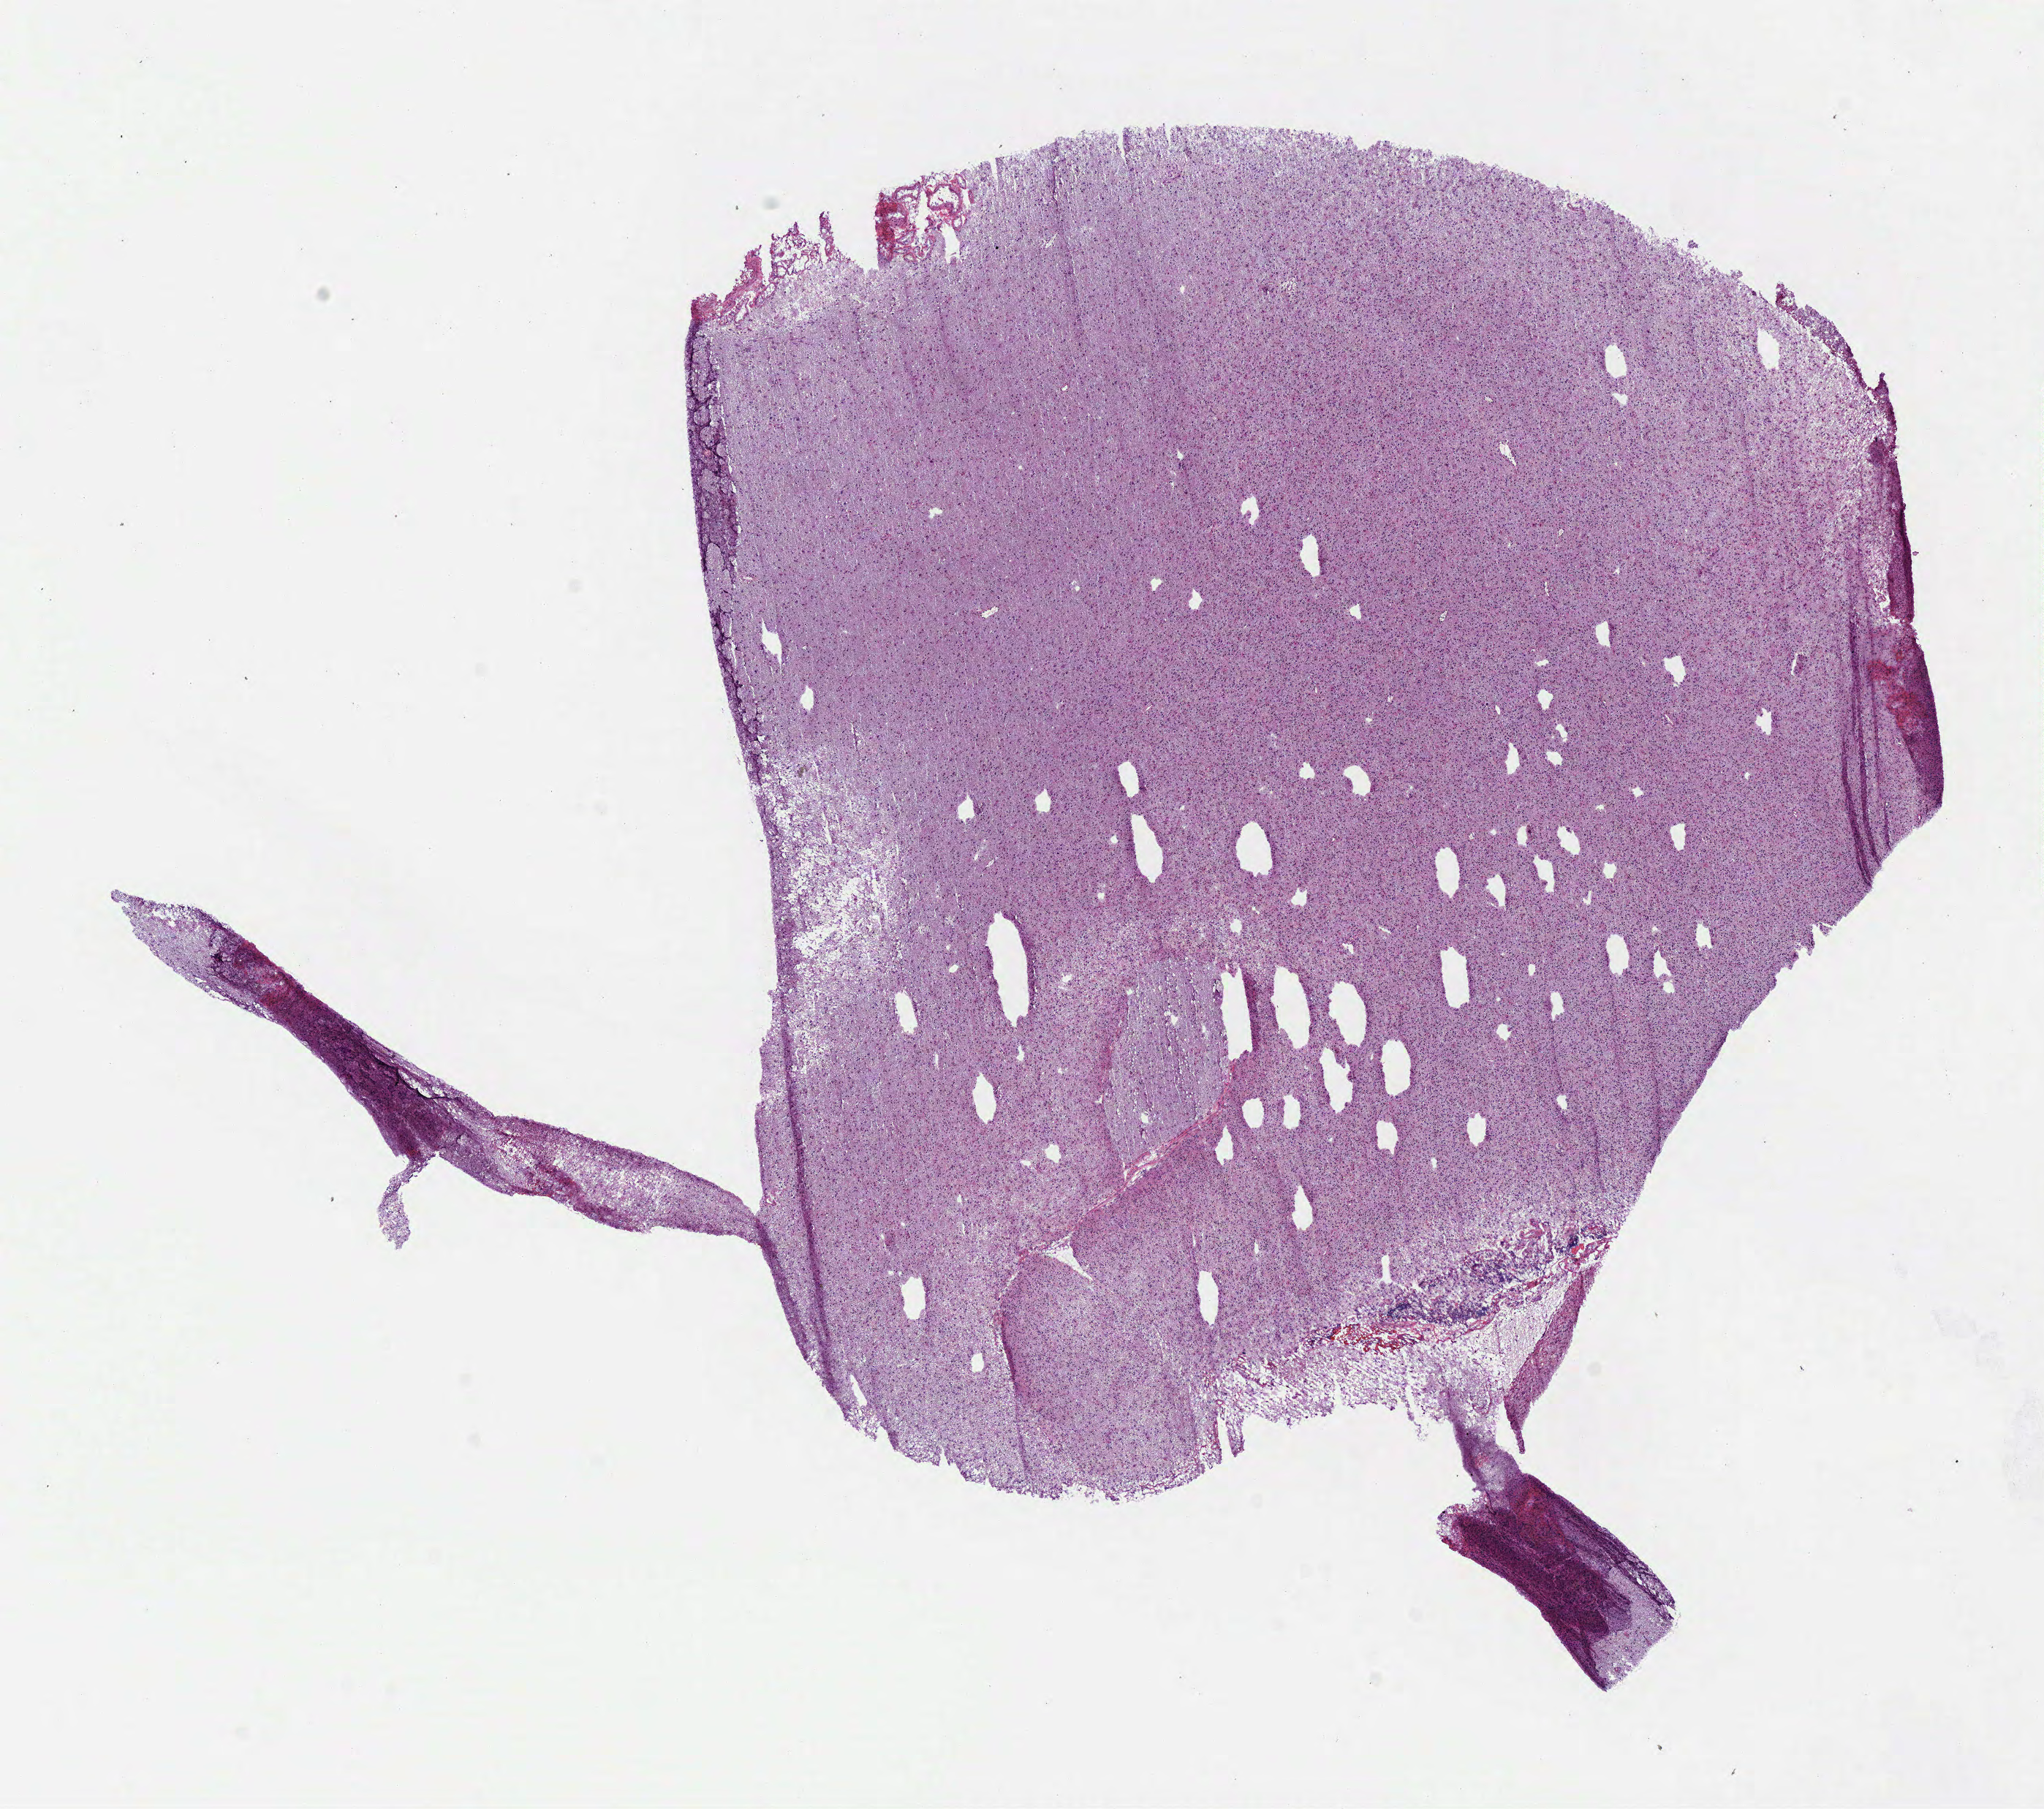
Hematoxylin and eosin (H&E) stained whole-slide image — shown as a low-resolution overview of the whole scanned area (about 11.0 x 9.7 mm), frozen section, primary tumour sample from the brain. Female patient; age at initial diagnosis 61 years. Histologic grade: G3 (poorly differentiated). Slide review estimates, as recorded: tumour cells 100%, tumour nuclei 75%, normal cells 0%, stromal cells 0%, necrosis 0%.
Pathologic diagnosis: Mixed glioma.